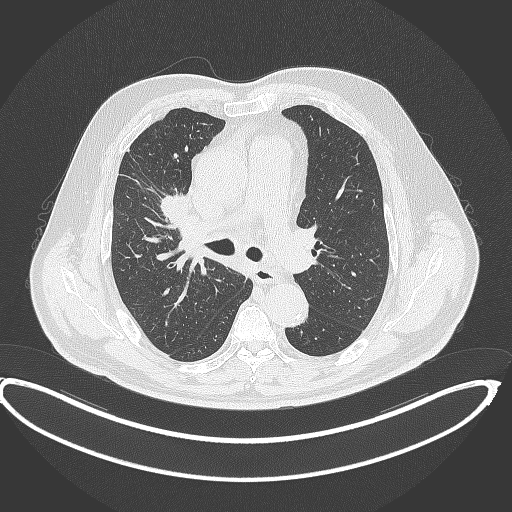
Chest CT, one axial slice. Position 258 of 390 along the scan axis. 120 kVp. Lung window (W 1500 / L -600 HU). 1 mm slice thickness. 512 × 512 image matrix. Male patient, age 62 years. From the clinical record (not read from this slice): clinical TNM (as recorded): T1c N3 M1c.
Structures marked on this image (rectangle marked by the reading radiologist):
- lung tumour (recorded histology: adenocarcinoma): bounding box (x1, y1, x2, y2) in pixels: (158, 193, 191, 221)